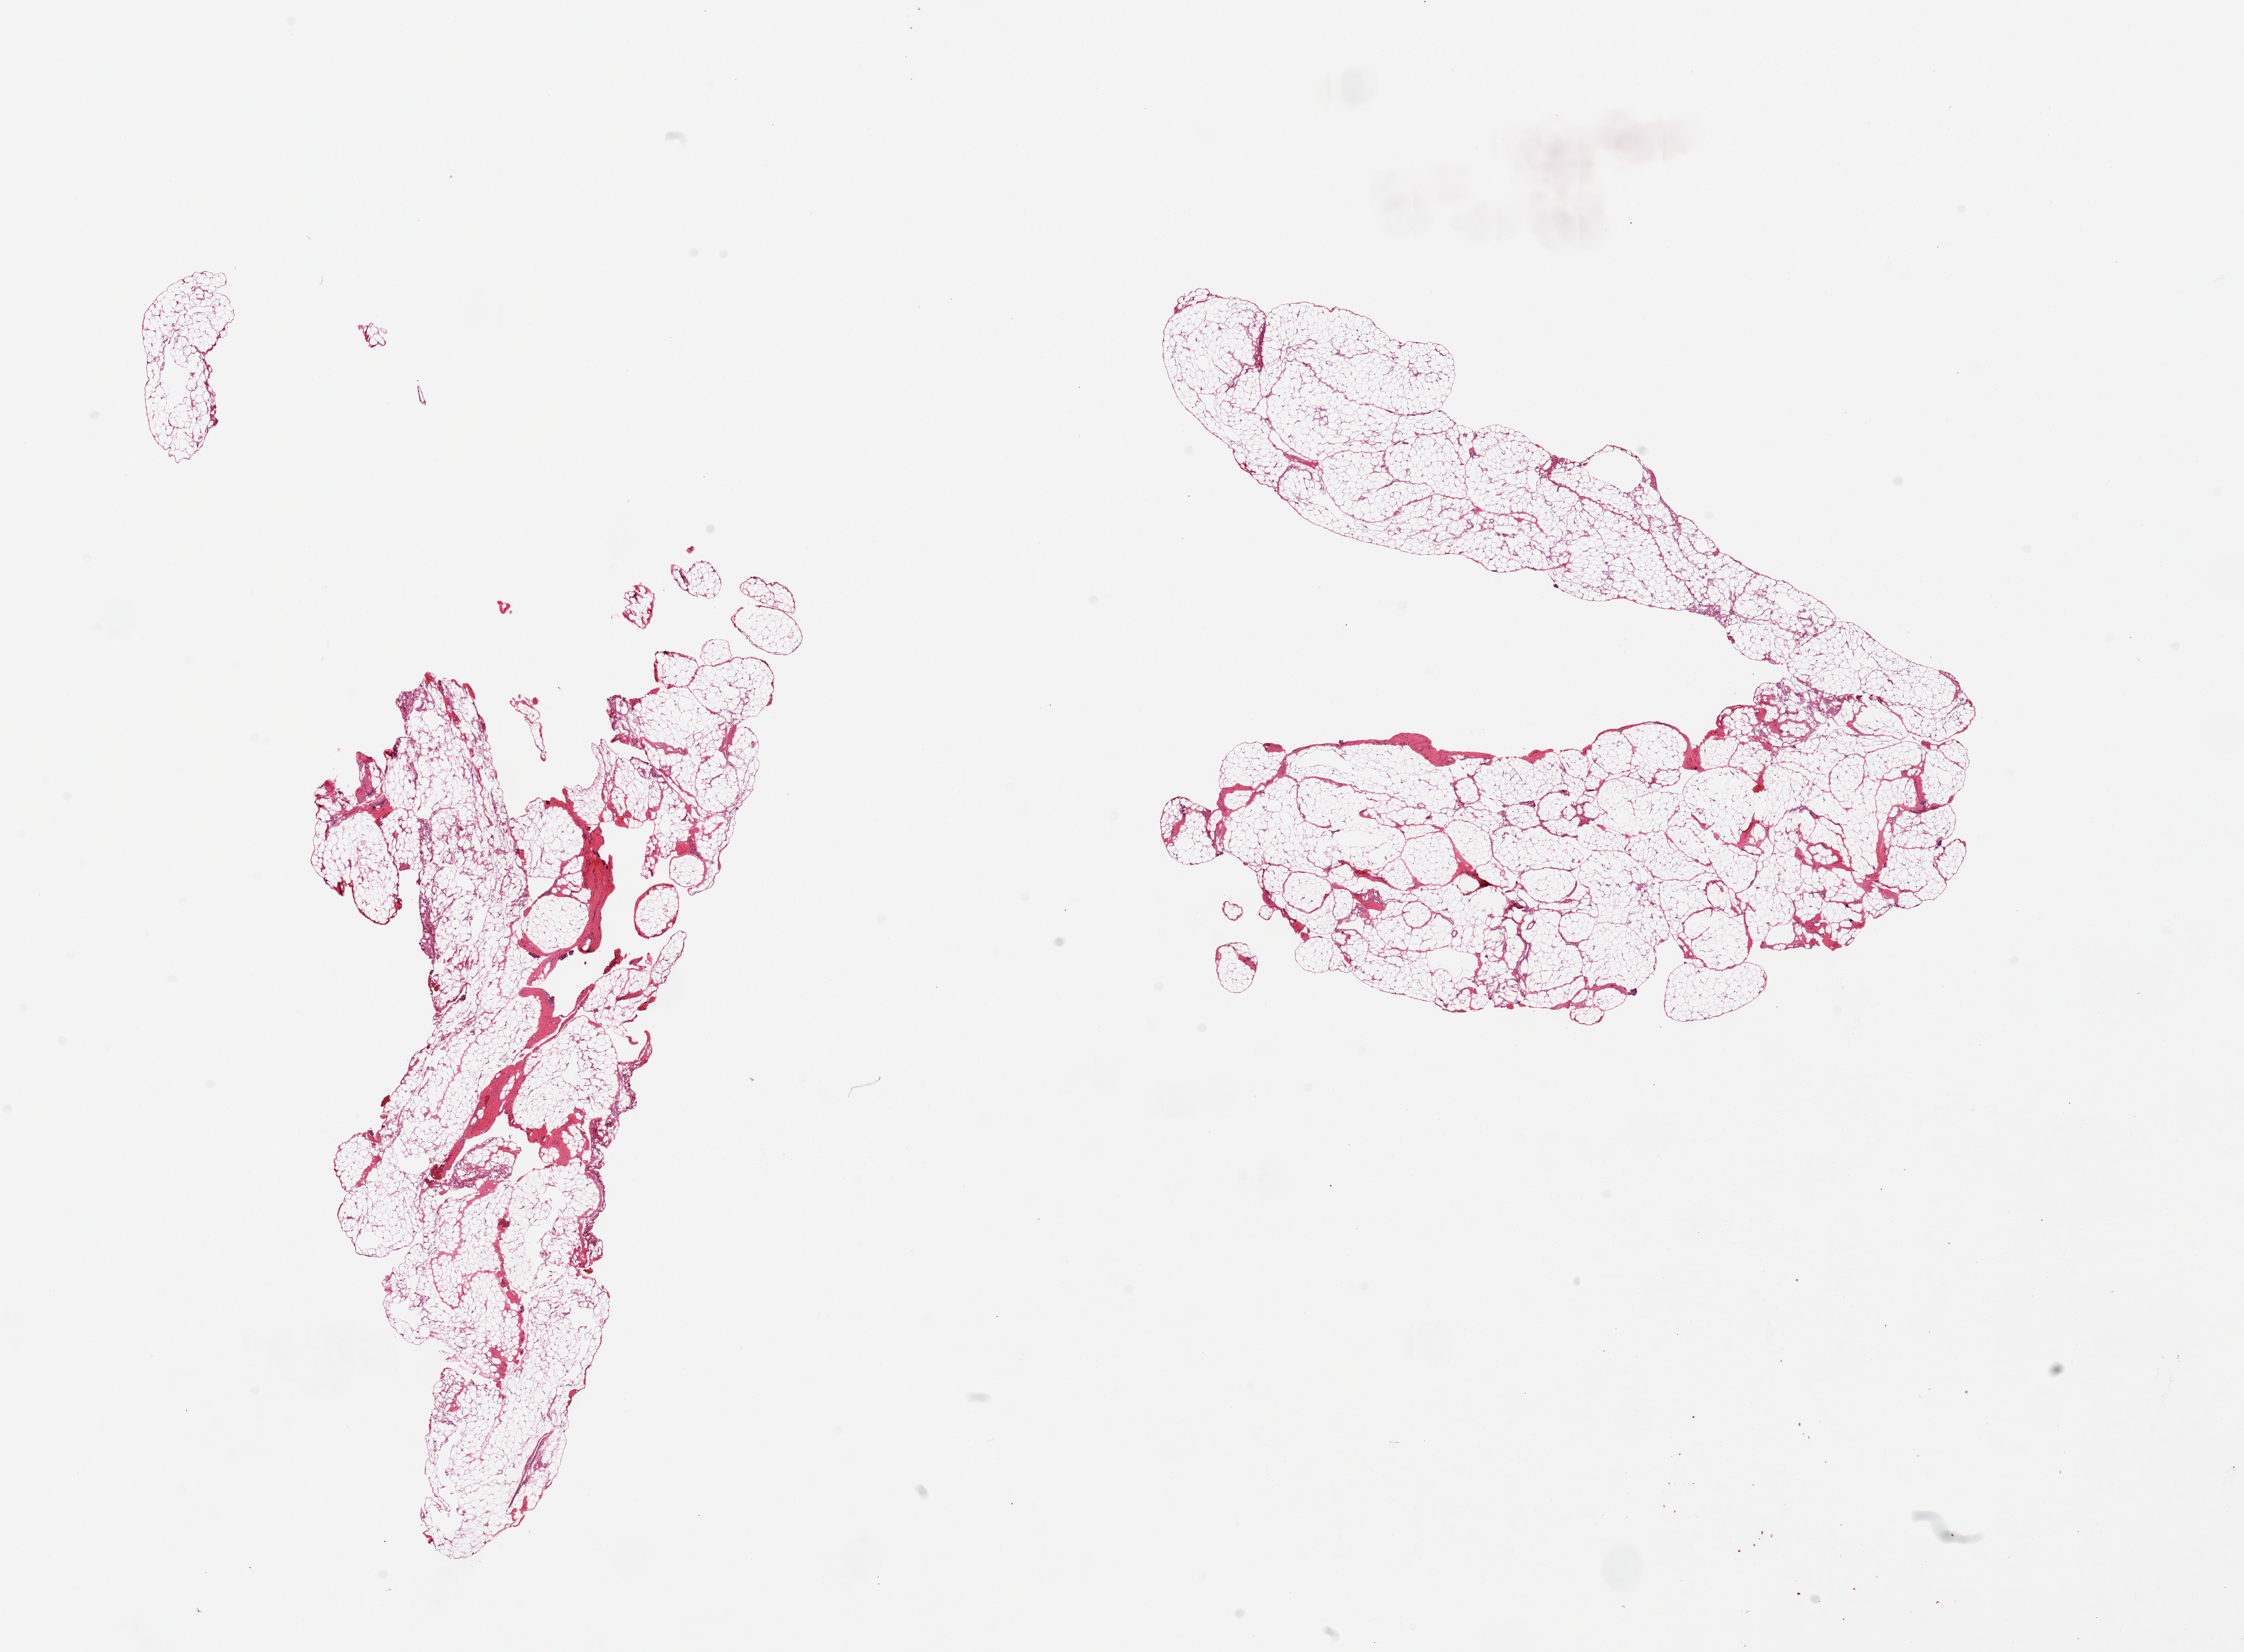
Digitized H&E-stained section, low-resolution overview of the scanned area, about 26.6 x 19.6 mm (acquisition: 20x scan), PAXgene-fixed, paraffin-embedded tissue, sampled site (target tissue): omentum, tissue donor sample. Donor: female.
Pathologist's review note for this sample: 2 pieces.